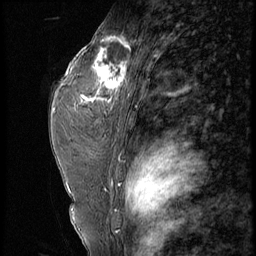
Breast MRI (dynamic contrast-enhanced), one sagittal slice. Position 37 of 56 along the scan axis. 4 images stored at this slice position (order not interpretable as contrast timing). 1.5 T. TE 4.2 ms, TR 9 ms. 2.5 mm slice thickness. 256 × 256 image matrix, field of view 180 × 180 mm. Patient: female, 44 years. Case-level facts recorded for this patient, not image findings: setting: breast cancer imaged before/during neoadjuvant chemotherapy; receptor status: triple-negative.
Outlined on this slice (semi-automatic segmentation, software-assisted and operator-edited):
- analysis volume of interest (the breast-tissue region the enhancement analysis was run in; not a lesion): box from (x=87, y=28) to (x=132, y=99) px
- tumour enhancement mask (voxels above the 140 % enhancement threshold inside the analysis volume of interest): (x=91, y=36)–(x=131, y=99)